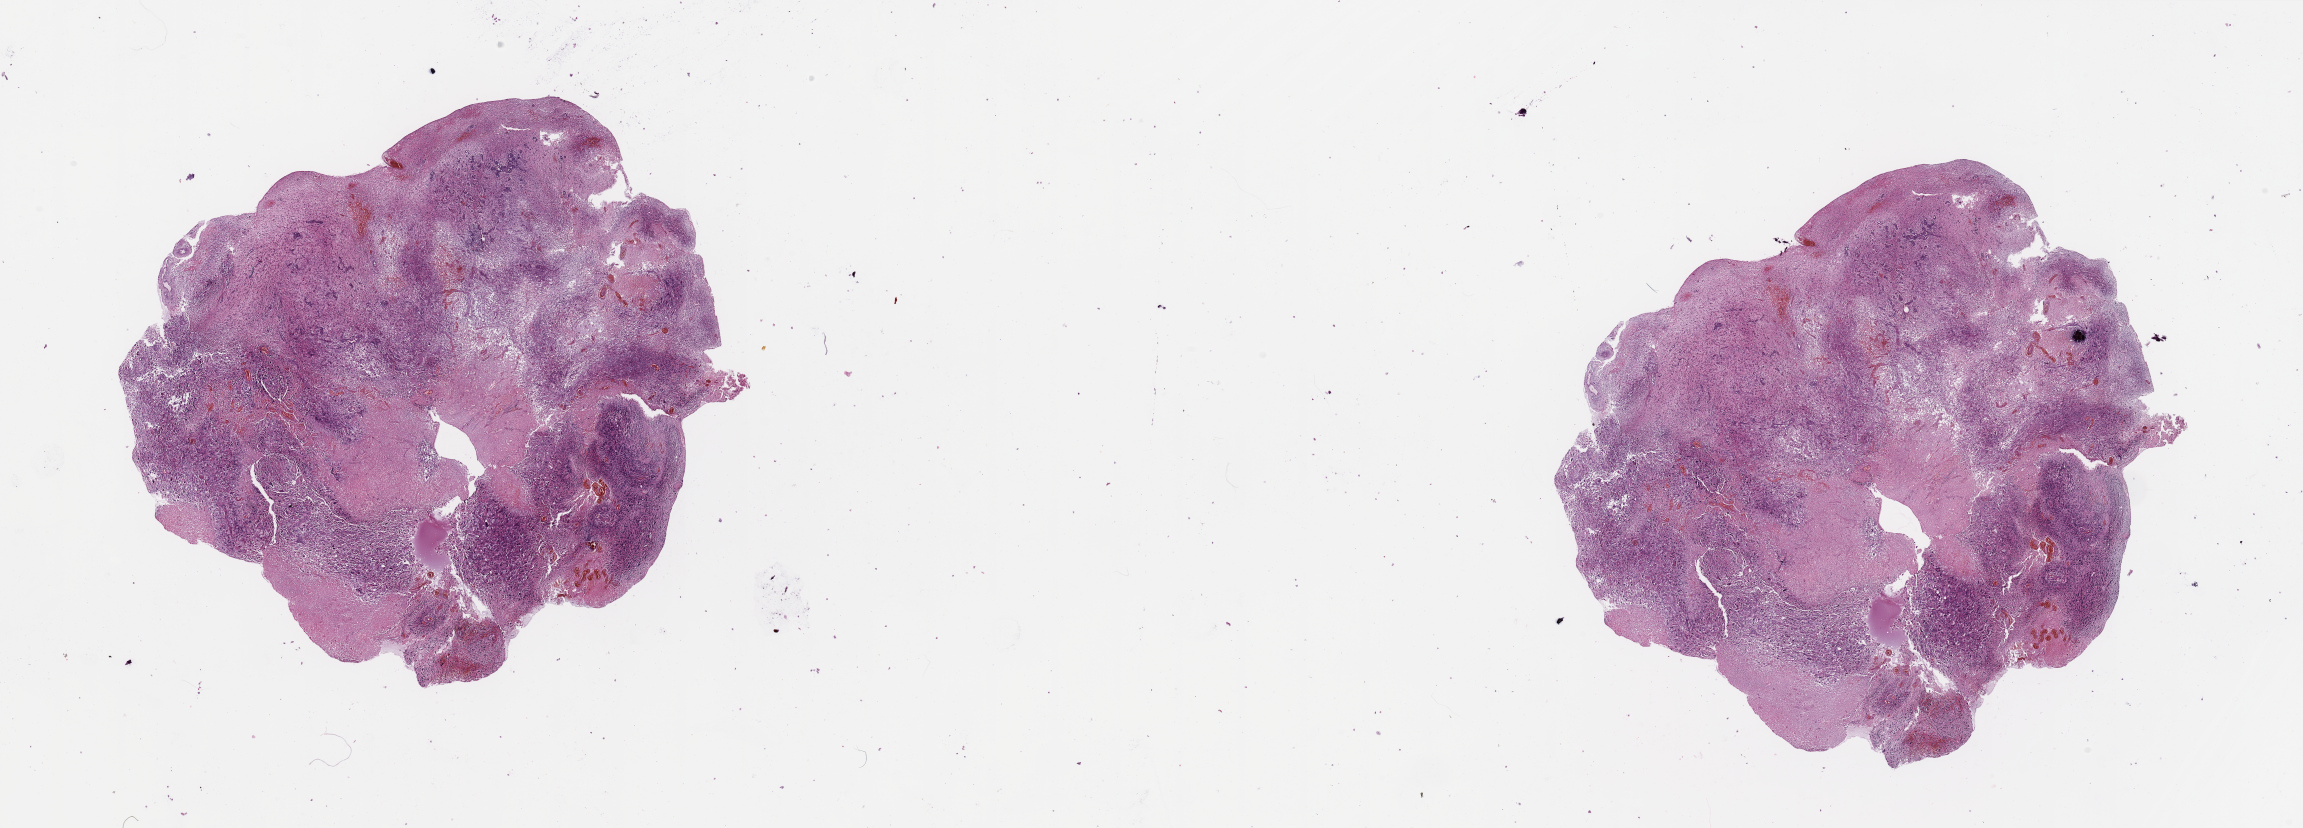
Digitized H&E-stained tissue section (whole slide) — low-resolution overview of the scanned area, about 36.4 x 13.1 mm (acquisition: 20x scan); tumour tissue sample, brain. Patient: male, age 77 years.
Diagnosis: Glioblastoma. Primary tumour site (as recorded): frontal lobe.